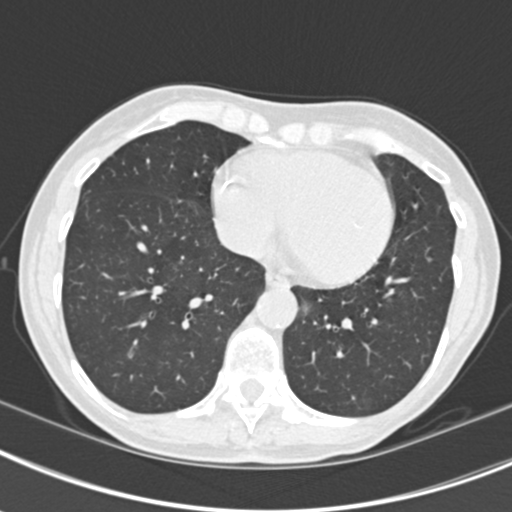
Chest CT (low-dose screening protocol), one axial image. Second screening round (one year after baseline). Lung window (W 1500 / L -600 HU). 2 mm slice thickness. Female participant, aged 63 years at enrolment. Current smoker at enrolment.
Expert reader's lesion annotation, box from (x=111, y=326) to (x=155, y=370) px. The screening reader recorded 9 non-calcified nodules or masses ≥4 mm on this exam (left upper lobe, right upper lobe, left upper lobe, left lower lobe, right middle lobe, left lower lobe, left lower lobe, right lower lobe, right lower lobe); which of them this box marks is not recorded. Lung cancer was diagnosed 408 days after this screen (after the third annual screen): bronchiolo-alveolar adenocarcinoma, NOS, right upper lobe, right middle lobe, right lower lobe, left upper lobe, left lower lobe, moderately differentiated (G2), stage IV (AJCC 6th edition).